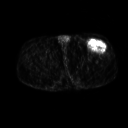
FDG PET of an extremity soft-tissue mass (from a PET/CT study), one axial slice; 3.27 mm slice thickness; 128 × 128 image matrix, field of view 500 × 500 mm. Patient: male, 64 years. From the clinical record (not read from this slice): histological type: extraskeletal osteosarcoma; grade: high; site of the primary tumour: thigh.
Structures marked on this image (expert contour drawn on MRI and transferred to this co-registered scan by the dataset authors):
- gross tumour volume (mass): bounding box <89,41,106,52> (left, top, right, bottom; pixels)